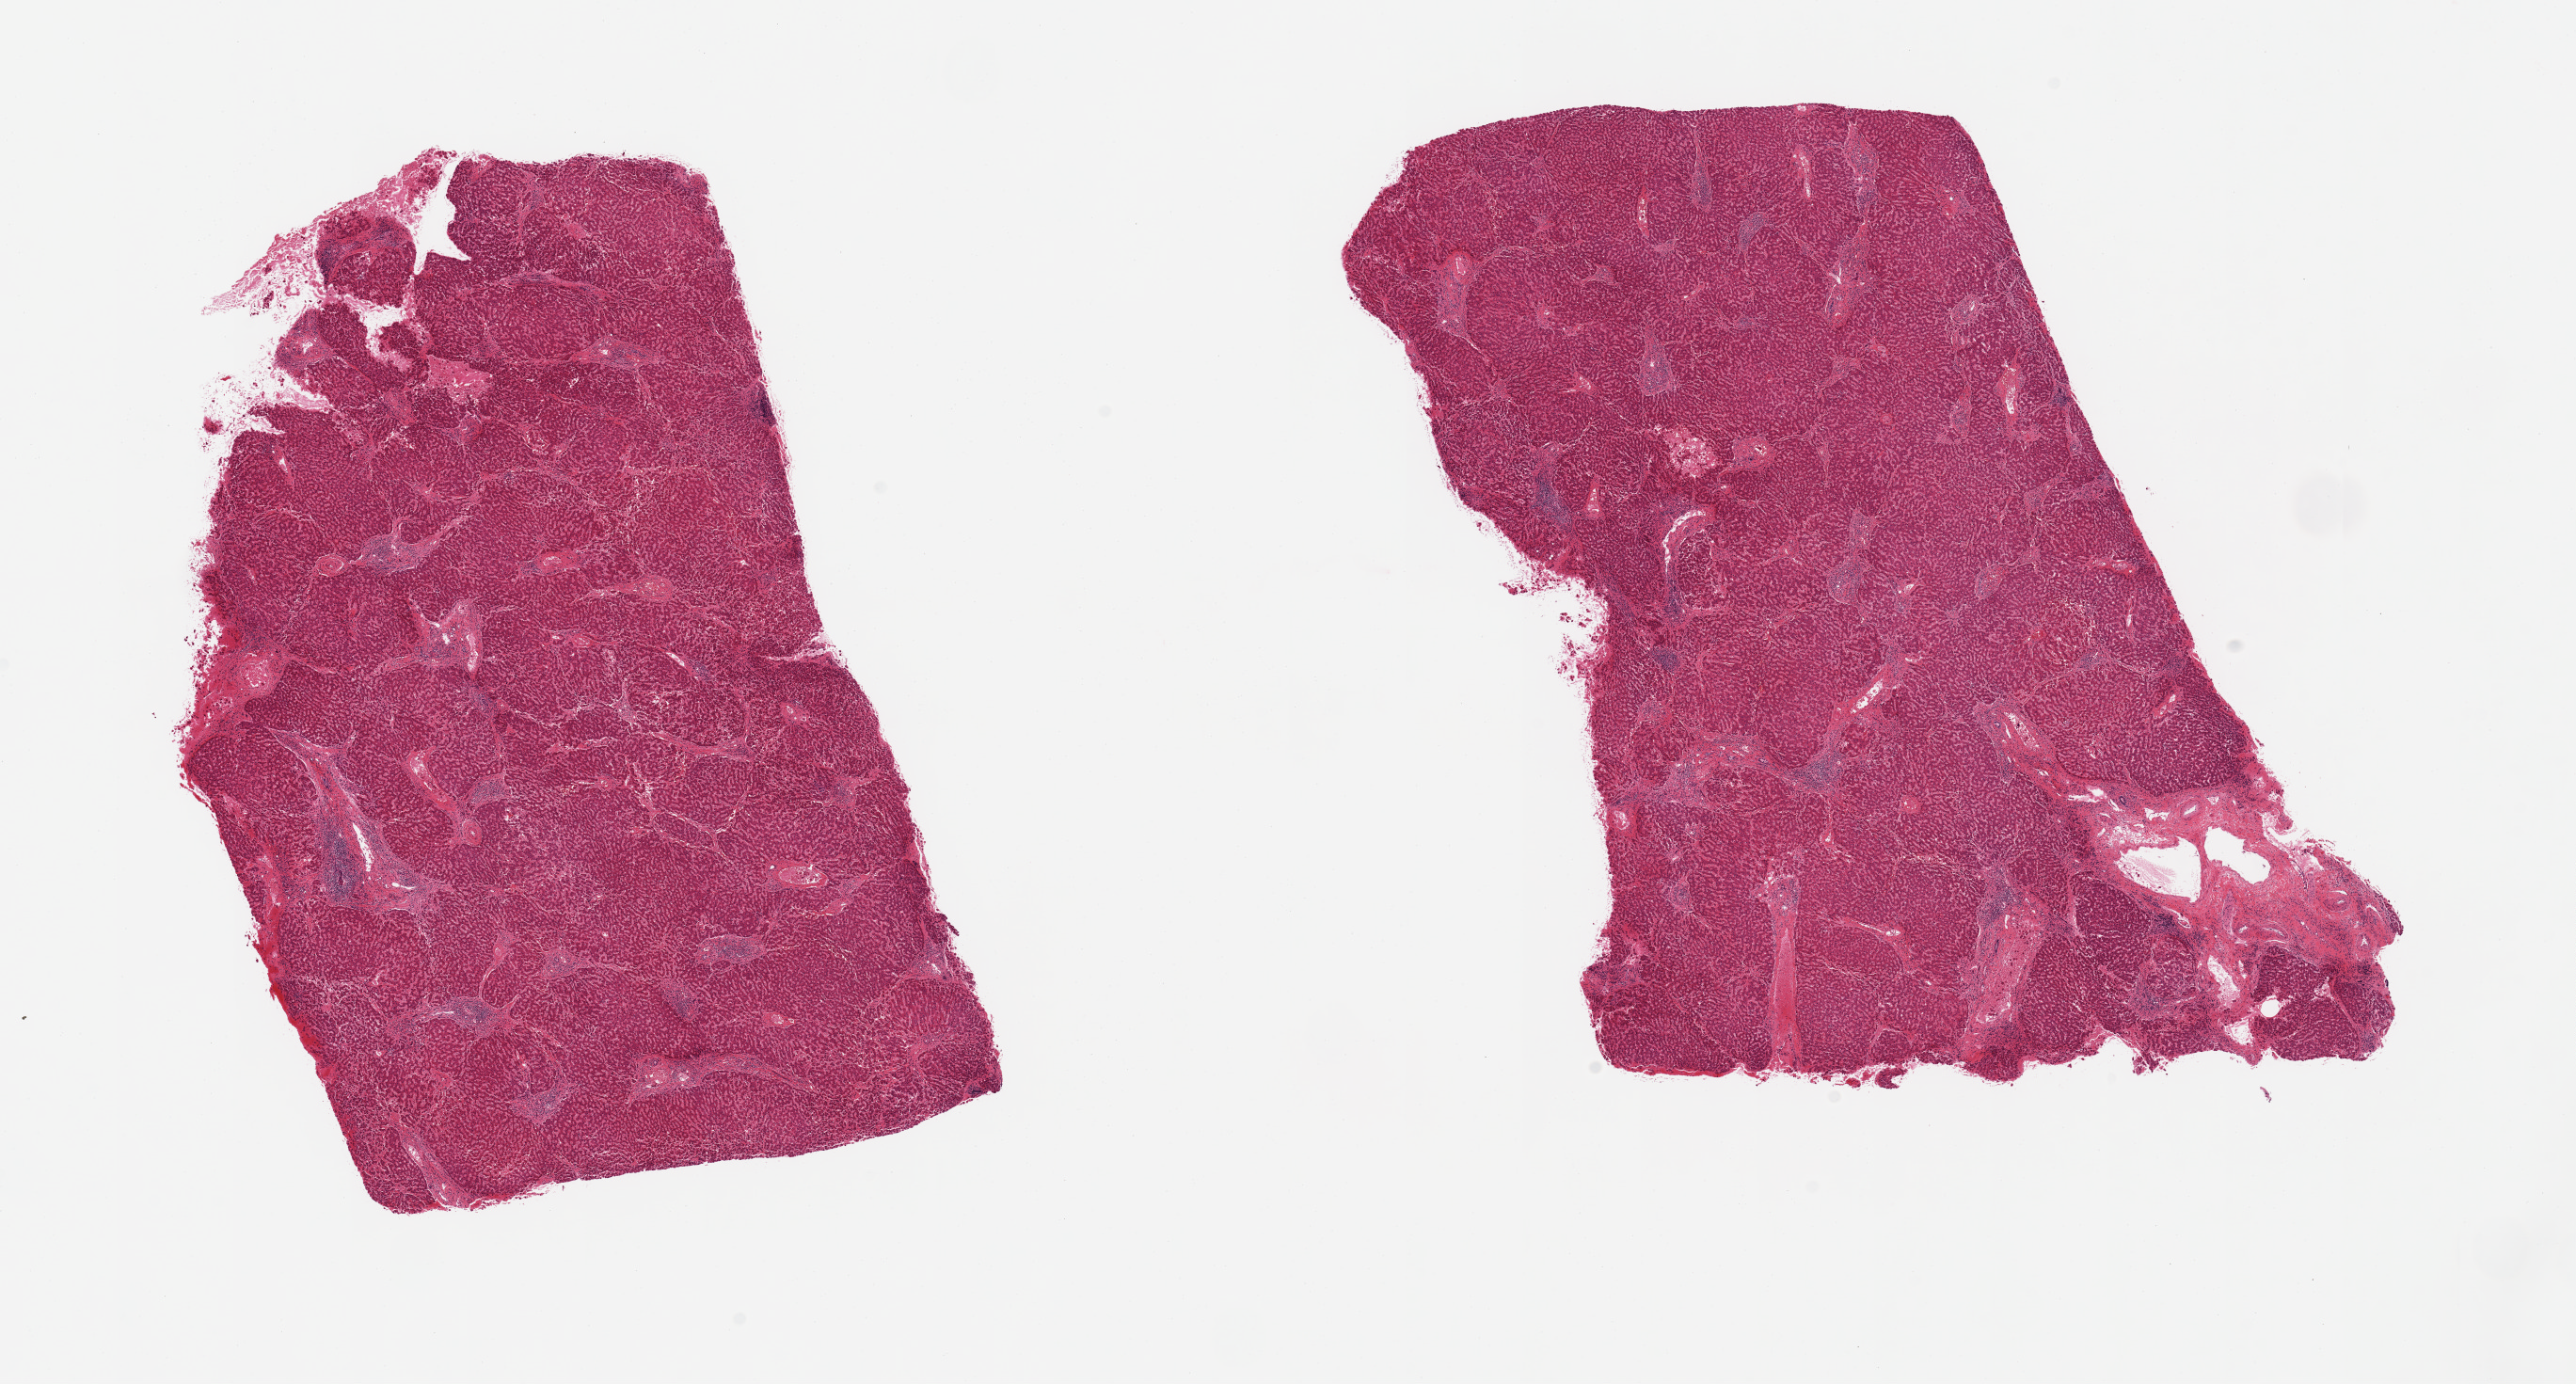
Digitized hematoxylin and eosin (H&E)-stained section, shown as a low-resolution overview of the whole scanned area (about 21.7 x 11.6 mm), PAXgene-fixed paraffin-embedded (PFPE) section, section of liver (target tissue), tissue donor sample.
- reviewer comment on this tissue sample: 2 pieces; periportal fibrosis with chronic inflammation and early bridging fibrosis